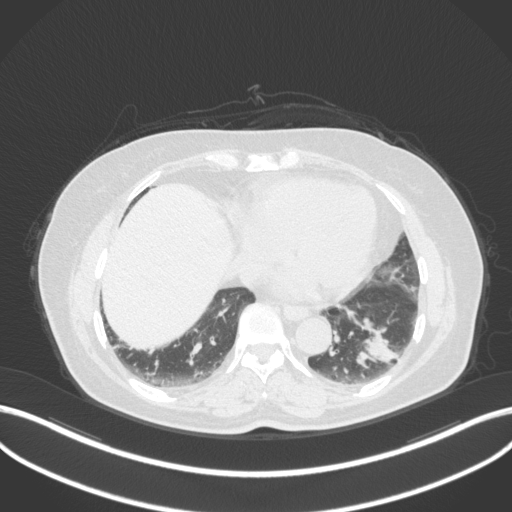
Chest CT, one axial slice; slice 122 of 307 in the series (ordered by position); reconstruction kernel B31f; 120 kVp; lung window (W 1500 / L -600 HU); 1 mm slice thickness; 512 × 512 image matrix, field of view 400 × 400 mm. Female patient, age 59 years. From the clinical record (not read from this slice): clinical TNM (as recorded): T2a N0 M0; histopathological grade: G2-3.
Structures marked on this image (rectangle marked by the reading radiologist):
- lung tumour (recorded histology: adenocarcinoma): bounding box [x1, y1, x2, y2] px = [347, 312, 402, 373]